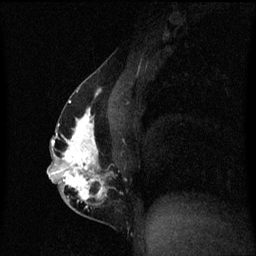
Breast MRI (dynamic contrast-enhanced), one sagittal slice. Slice 30 of 60 in the series (ordered by position). Dynamic contrast-enhanced series, image 2 of 3 at this slice position (ordered by acquisition). 1.5 T. TE 4.2 ms, TR 8.4 ms. 2 mm slice thickness. 256 × 256 image matrix, field of view 200 × 200 mm. Patient: female, 40 years.
Structures marked on this image (semi-automatic segmentation, software-assisted and operator-edited):
- analysis volume of interest (the breast-tissue region the enhancement analysis was run in; not a lesion): bounding box (x1, y1, x2, y2) in pixels: (48, 84, 121, 211)
- tumour enhancement mask (voxels above the 70 % enhancement threshold inside the analysis volume of interest): (48, 88, 107, 209)